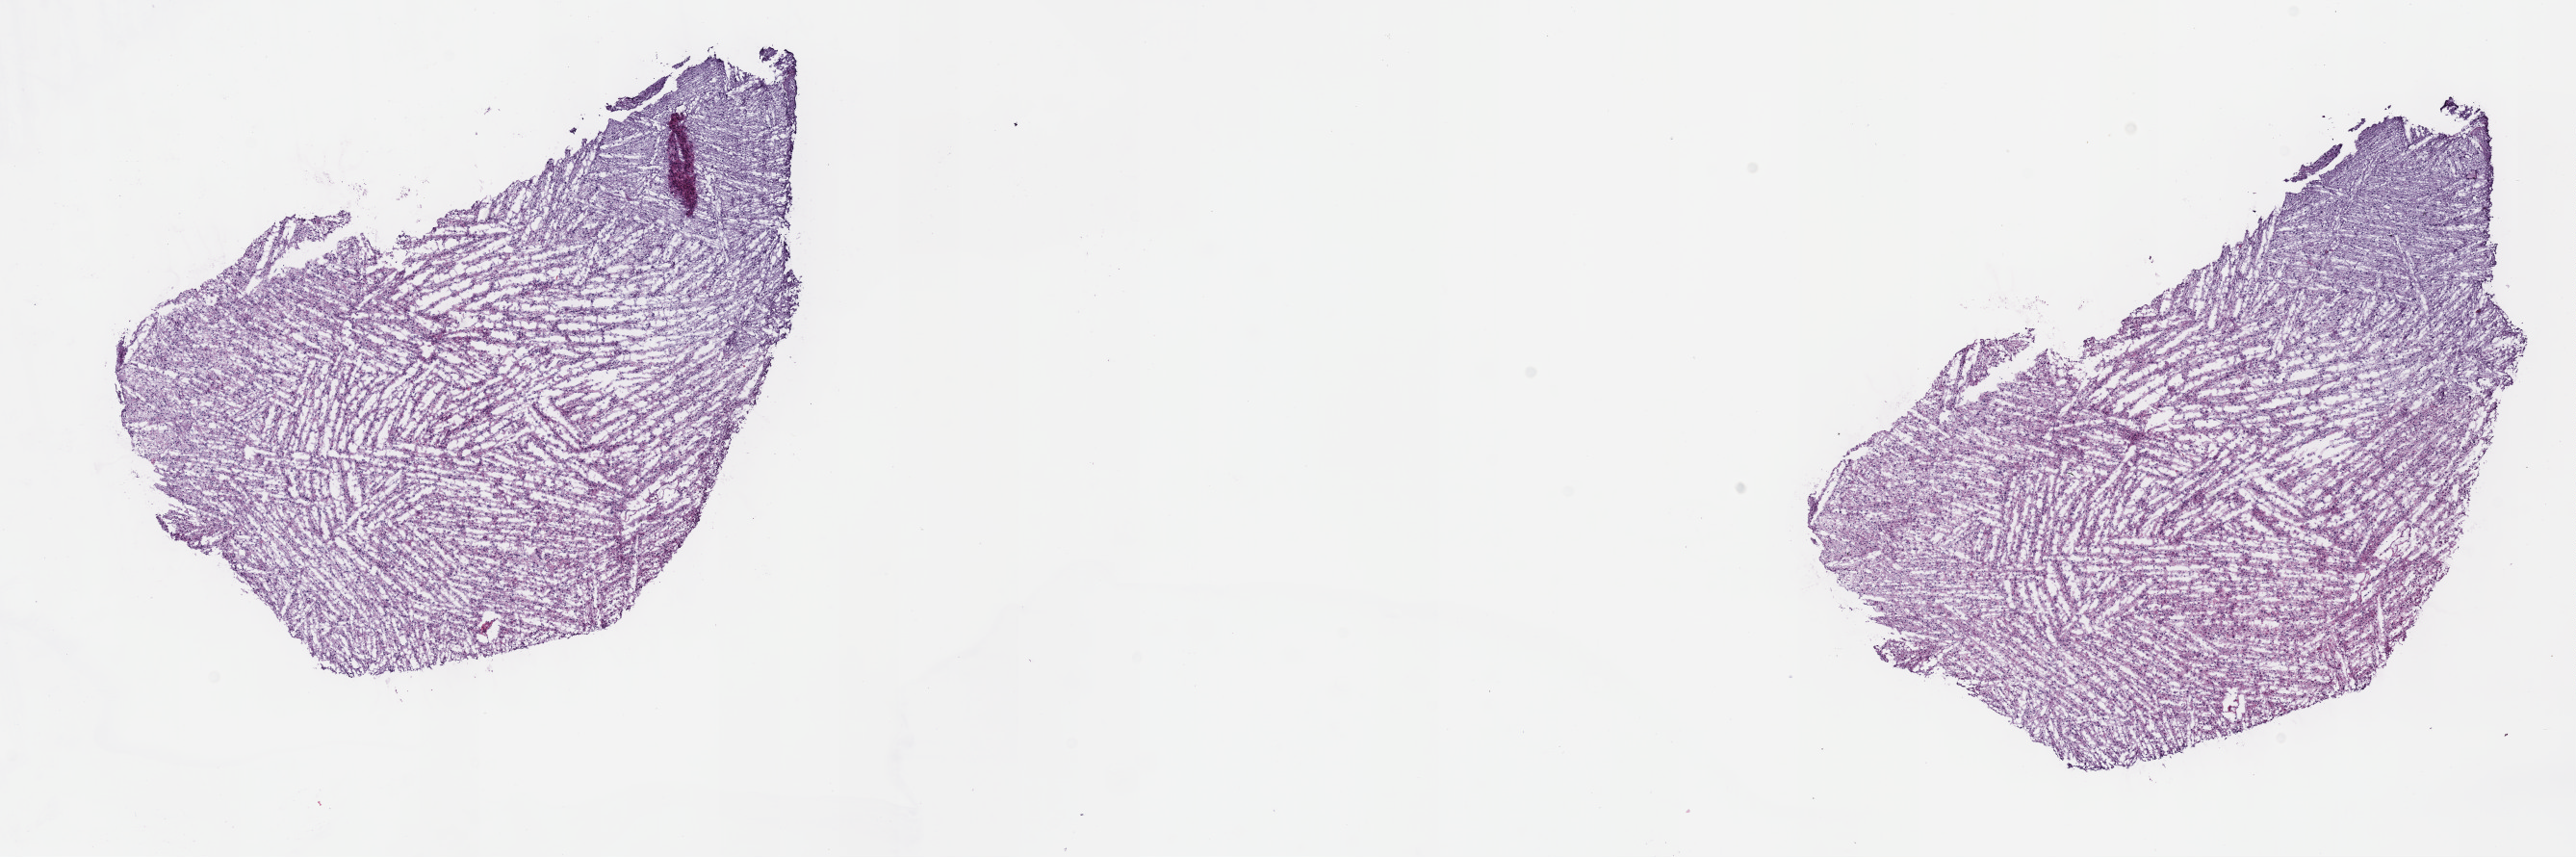
Hematoxylin and eosin (H&E) stained whole-slide image, shown as a low-resolution overview of the whole scanned area (about 21.6 x 7.2 mm); frozen section from the top of the tissue portion; brain, recurrent tumour sample. Male, age 29 years at initial diagnosis. Slide review estimates, as recorded: tumour cells 50%, tumour nuclei 85%, normal cells 10%, stromal cells 40%, necrosis 0%. Inflammatory infiltration, as recorded: lymphocyte infiltration 0%, monocyte infiltration 0%, neutrophil infiltration 0%.
This section: recurrent tumour. Patient diagnosis: Oligodendroglioma, NOS (cerebrum).